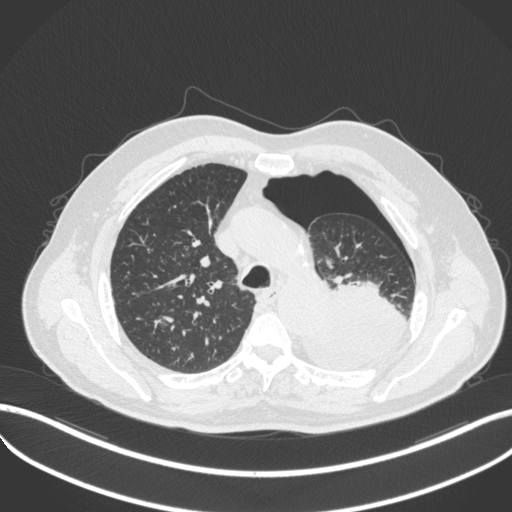
Chest CT, one axial slice. Position 371 of 466 along the scan axis. Reconstruction kernel B31f. 120 kVp. Lung window (W 1500 / L -600 HU). 512 × 512 image matrix, field of view 400 × 400 mm. Male patient, age 76 years. From the clinical record (not read from this slice): clinical TNM (as recorded): T3 N0 M1b.
Annotated regions visible in this slice (bounding box drawn by a radiologist):
- lung tumour (recorded histology: adenocarcinoma): bounding box (x1, y1, x2, y2) in pixels: (298, 281, 408, 371)